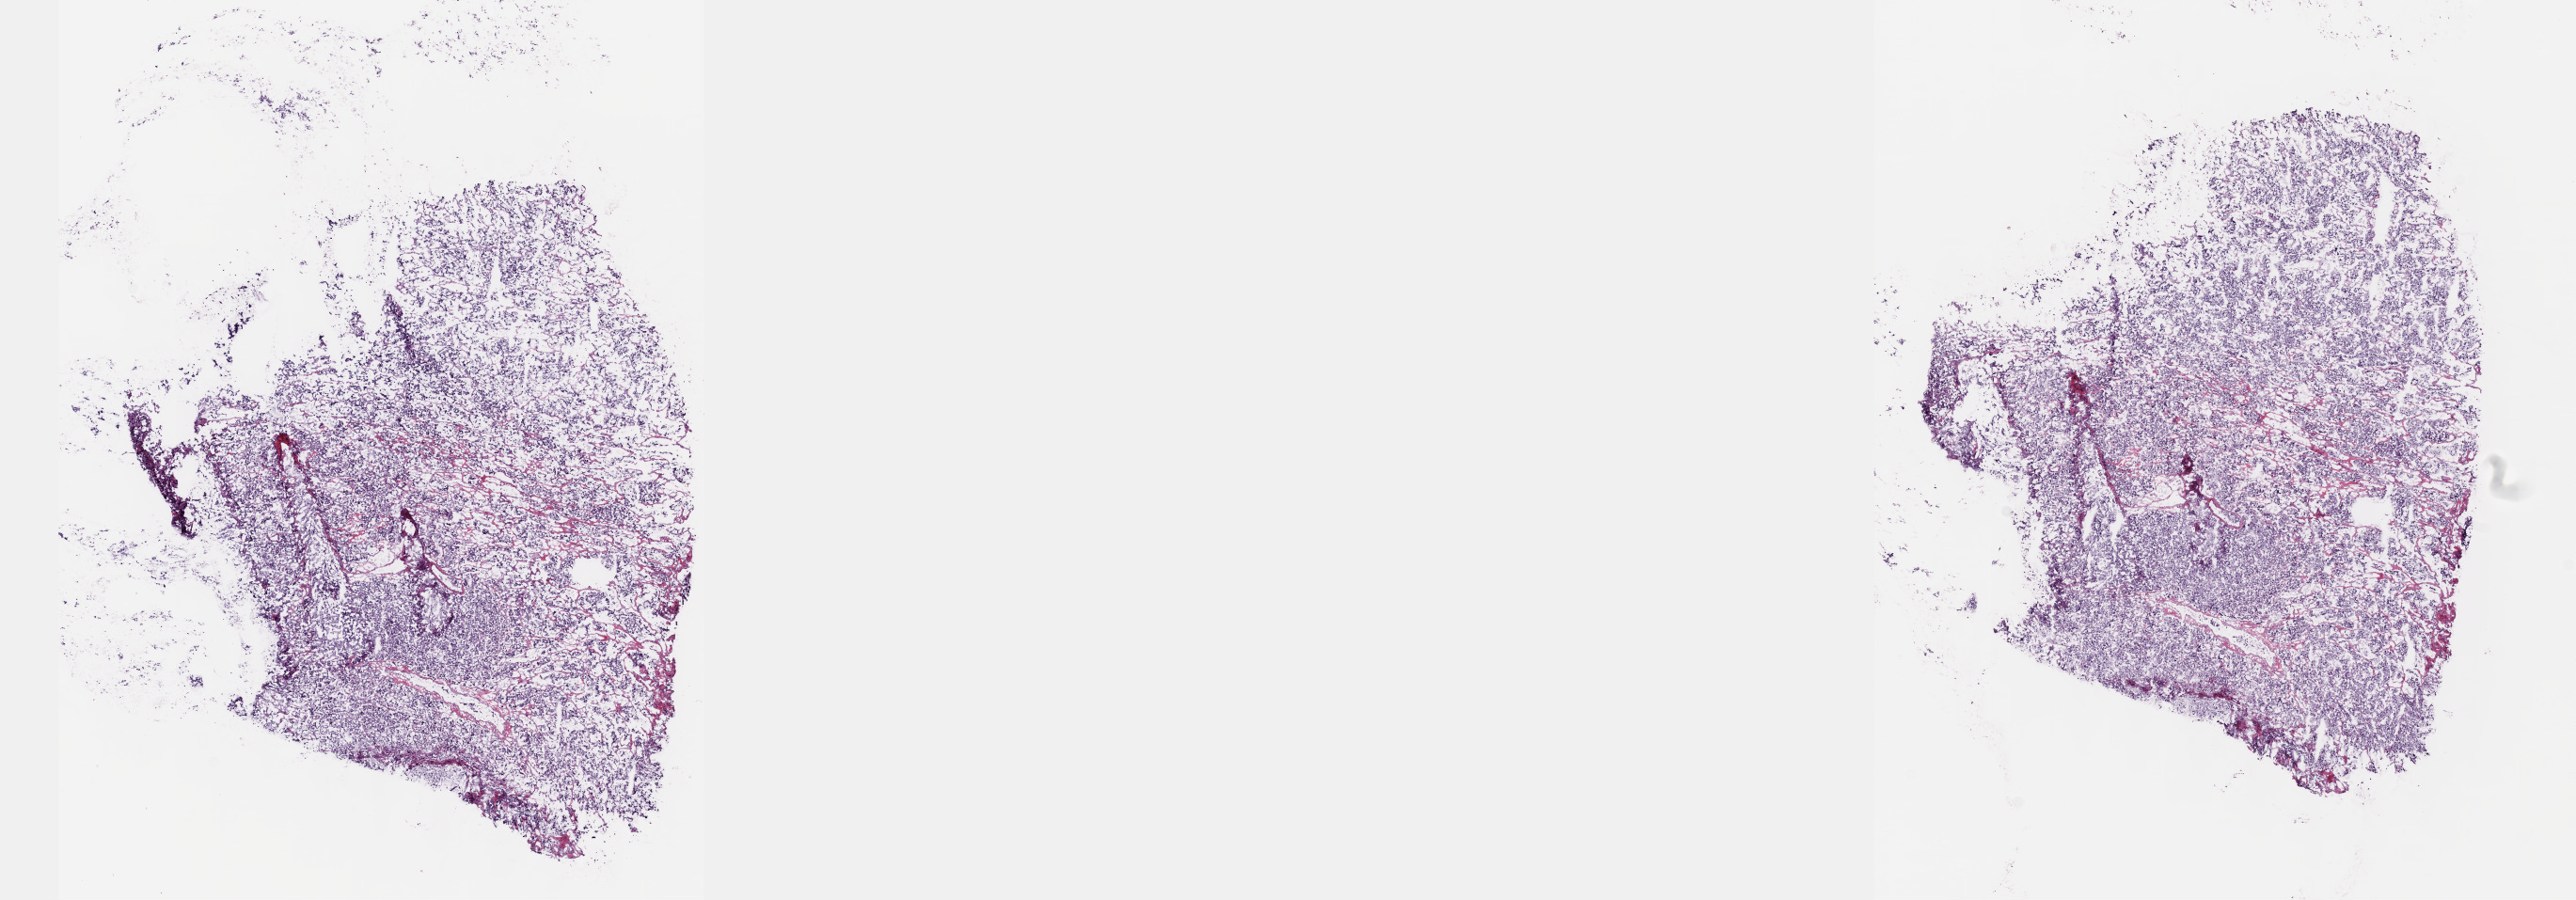
H&E whole-slide image — shown as a low-resolution overview of the whole scanned area (about 22.1 x 7.7 mm, slide scanned at 40x), frozen section, sample: primary tumour, adrenal gland. Female patient; age at initial diagnosis 32 years. Pathologist review of this section (percent, as recorded): tumour cells 100%, tumour nuclei 80%, normal cells 0%, stromal cells 0%, necrosis 0%. Infiltration values recorded for this section: lymphocyte infiltration 1%, monocyte infiltration 0%, neutrophil infiltration 0%.
Diagnosis: Pheochromocytoma, NOS.